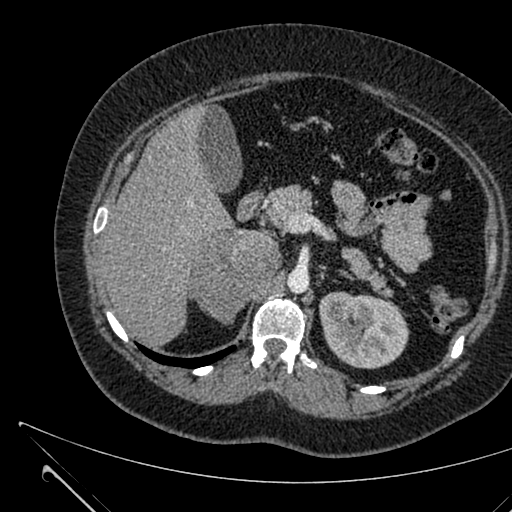
Contrast-enhanced abdominal CT, one axial slice. 120 kVp. Soft-tissue window (W 400 / L 40 HU). 1 mm slice thickness. 512 × 512 image matrix, field of view 376 × 376 mm. Patient: female, 36 years. Case-level facts recorded for this patient, not image findings: diagnosis: adrenocortical carcinoma; tumour side: right adrenal; tumour size at pathology: 10 cm; Ki-67 index: 20 %; stage (as recorded): 4.
Structures marked on this image (semi-automatic segmentation, software-assisted and operator-edited):
- mass: box from (x=192, y=232) to (x=277, y=322) px